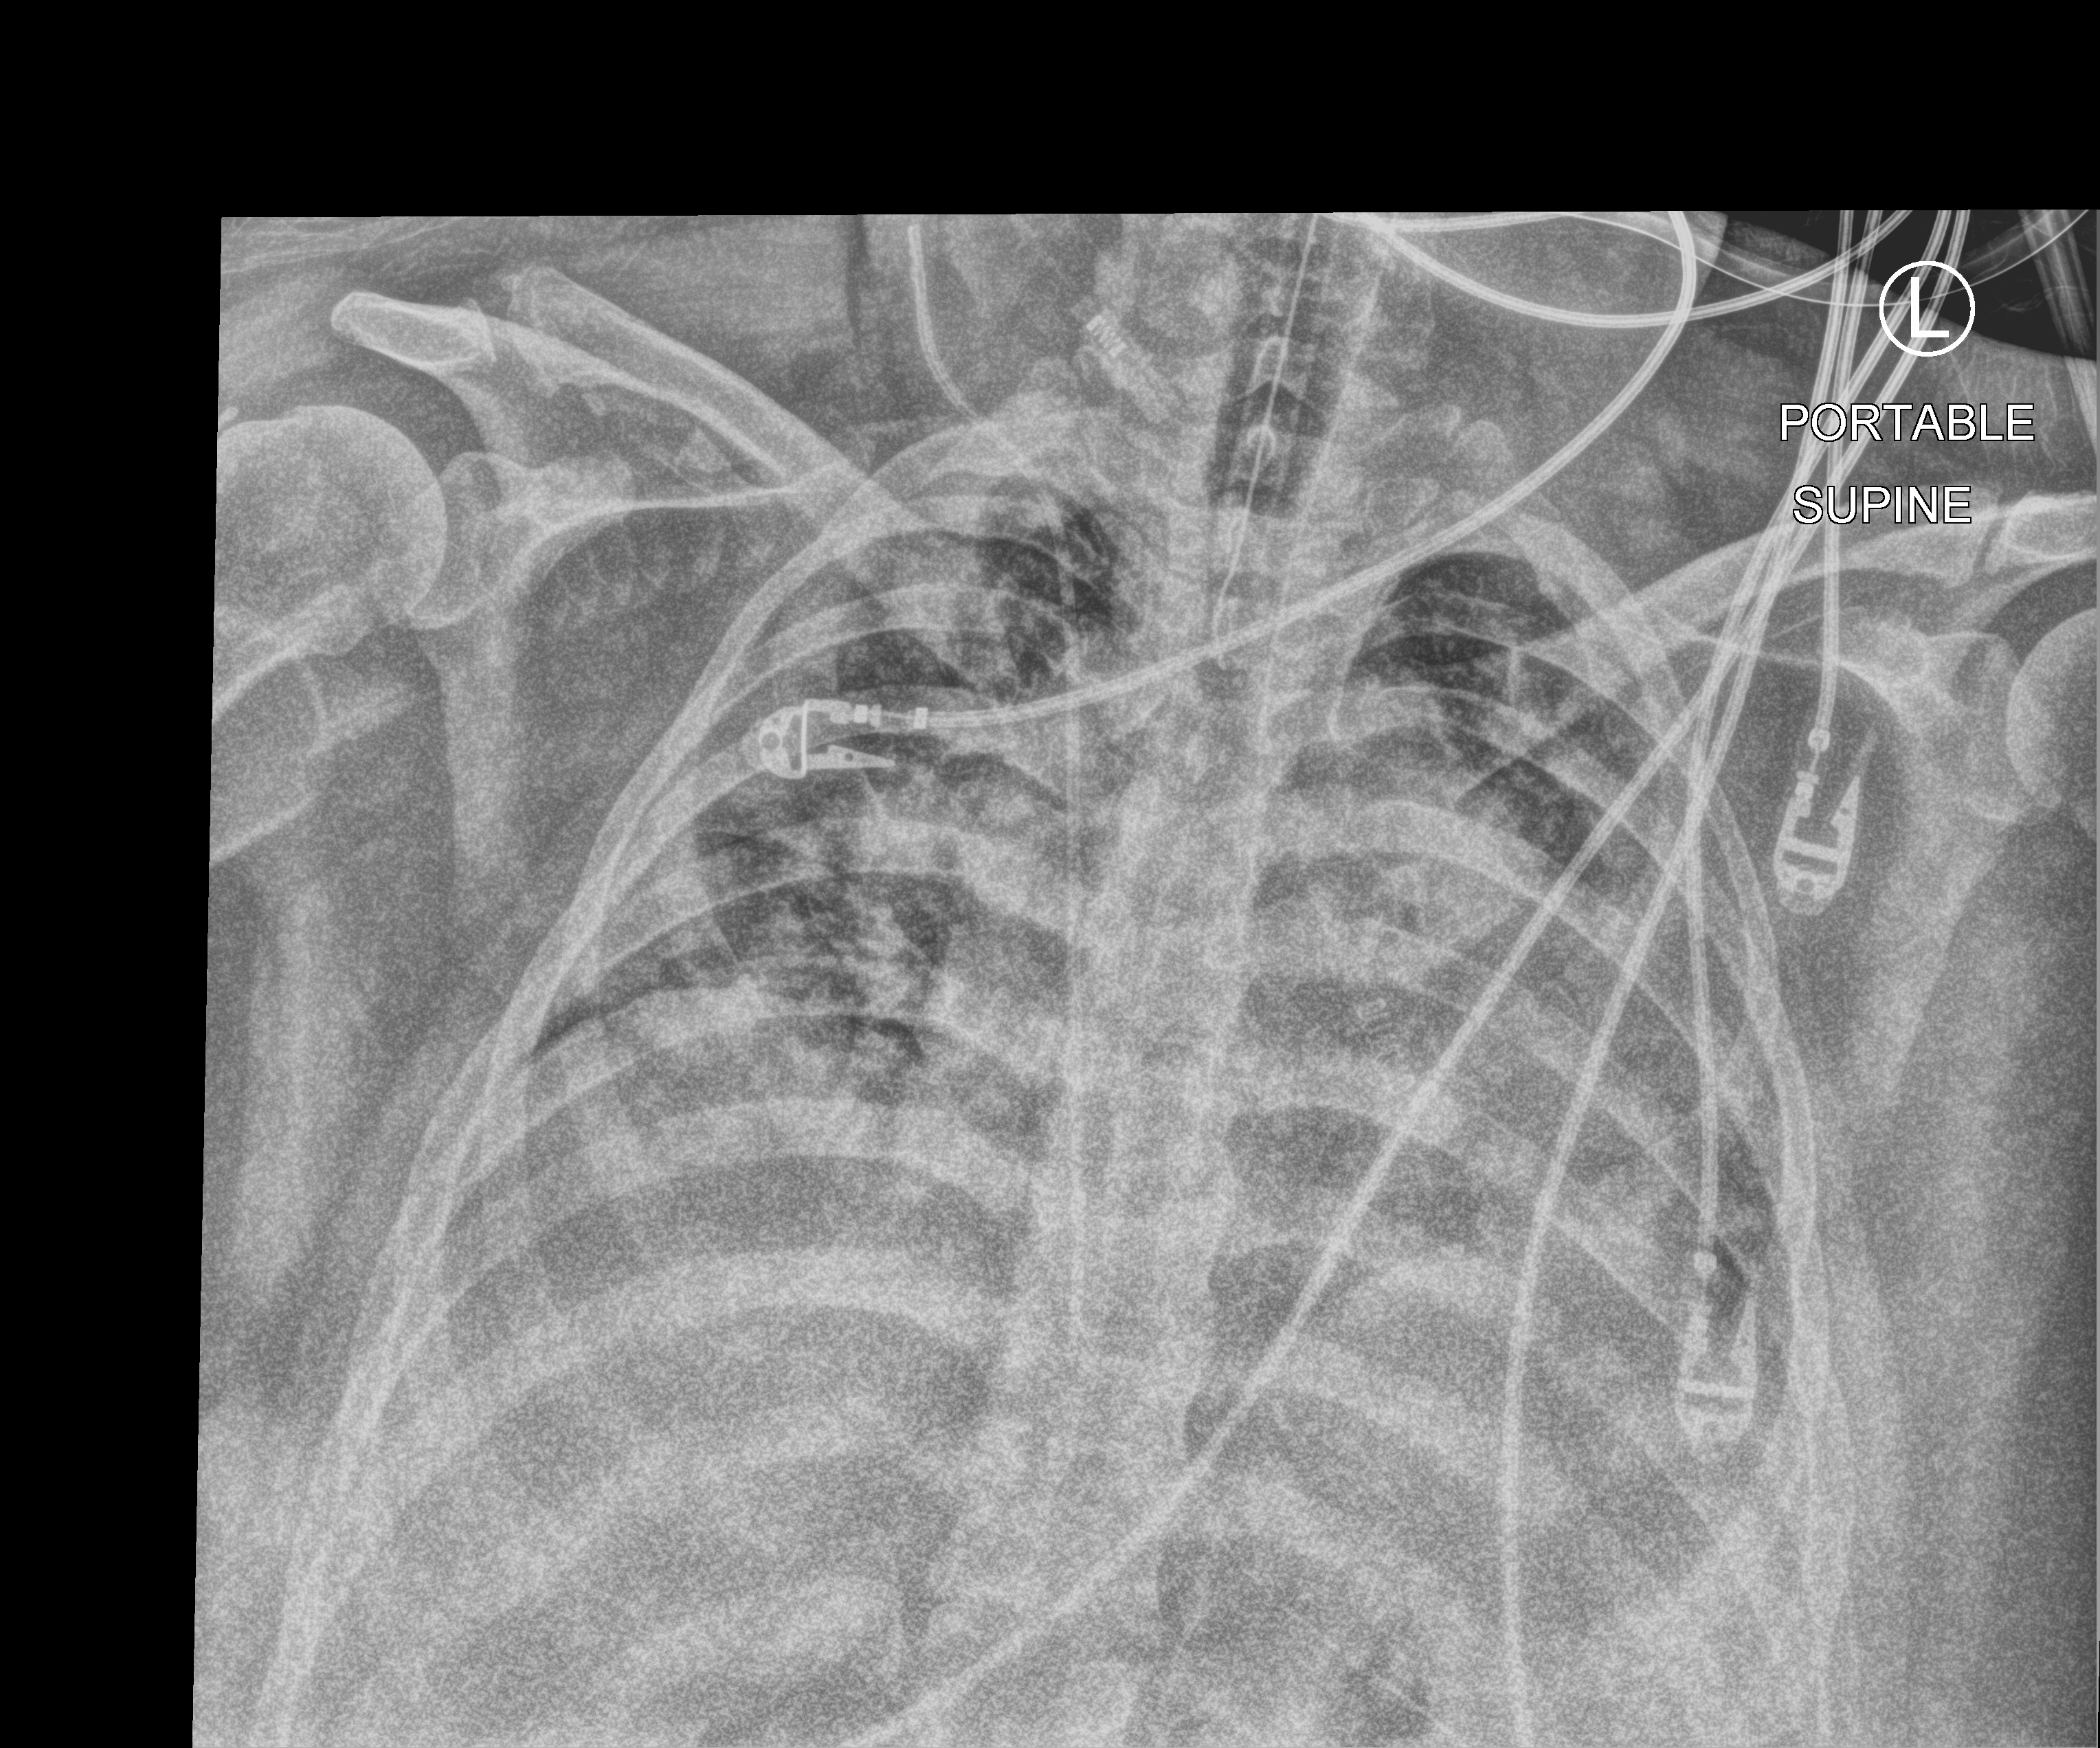
Portable chest radiograph; anteroposterior (AP) projection. Female patient hospitalised with COVID-19, age 18–59 years.
From the hospital-stay record, not from the radiograph (when in the stay this image was taken is not recorded): chronic kidney disease (admission record): no; mechanically ventilated during this hospital stay: yes.